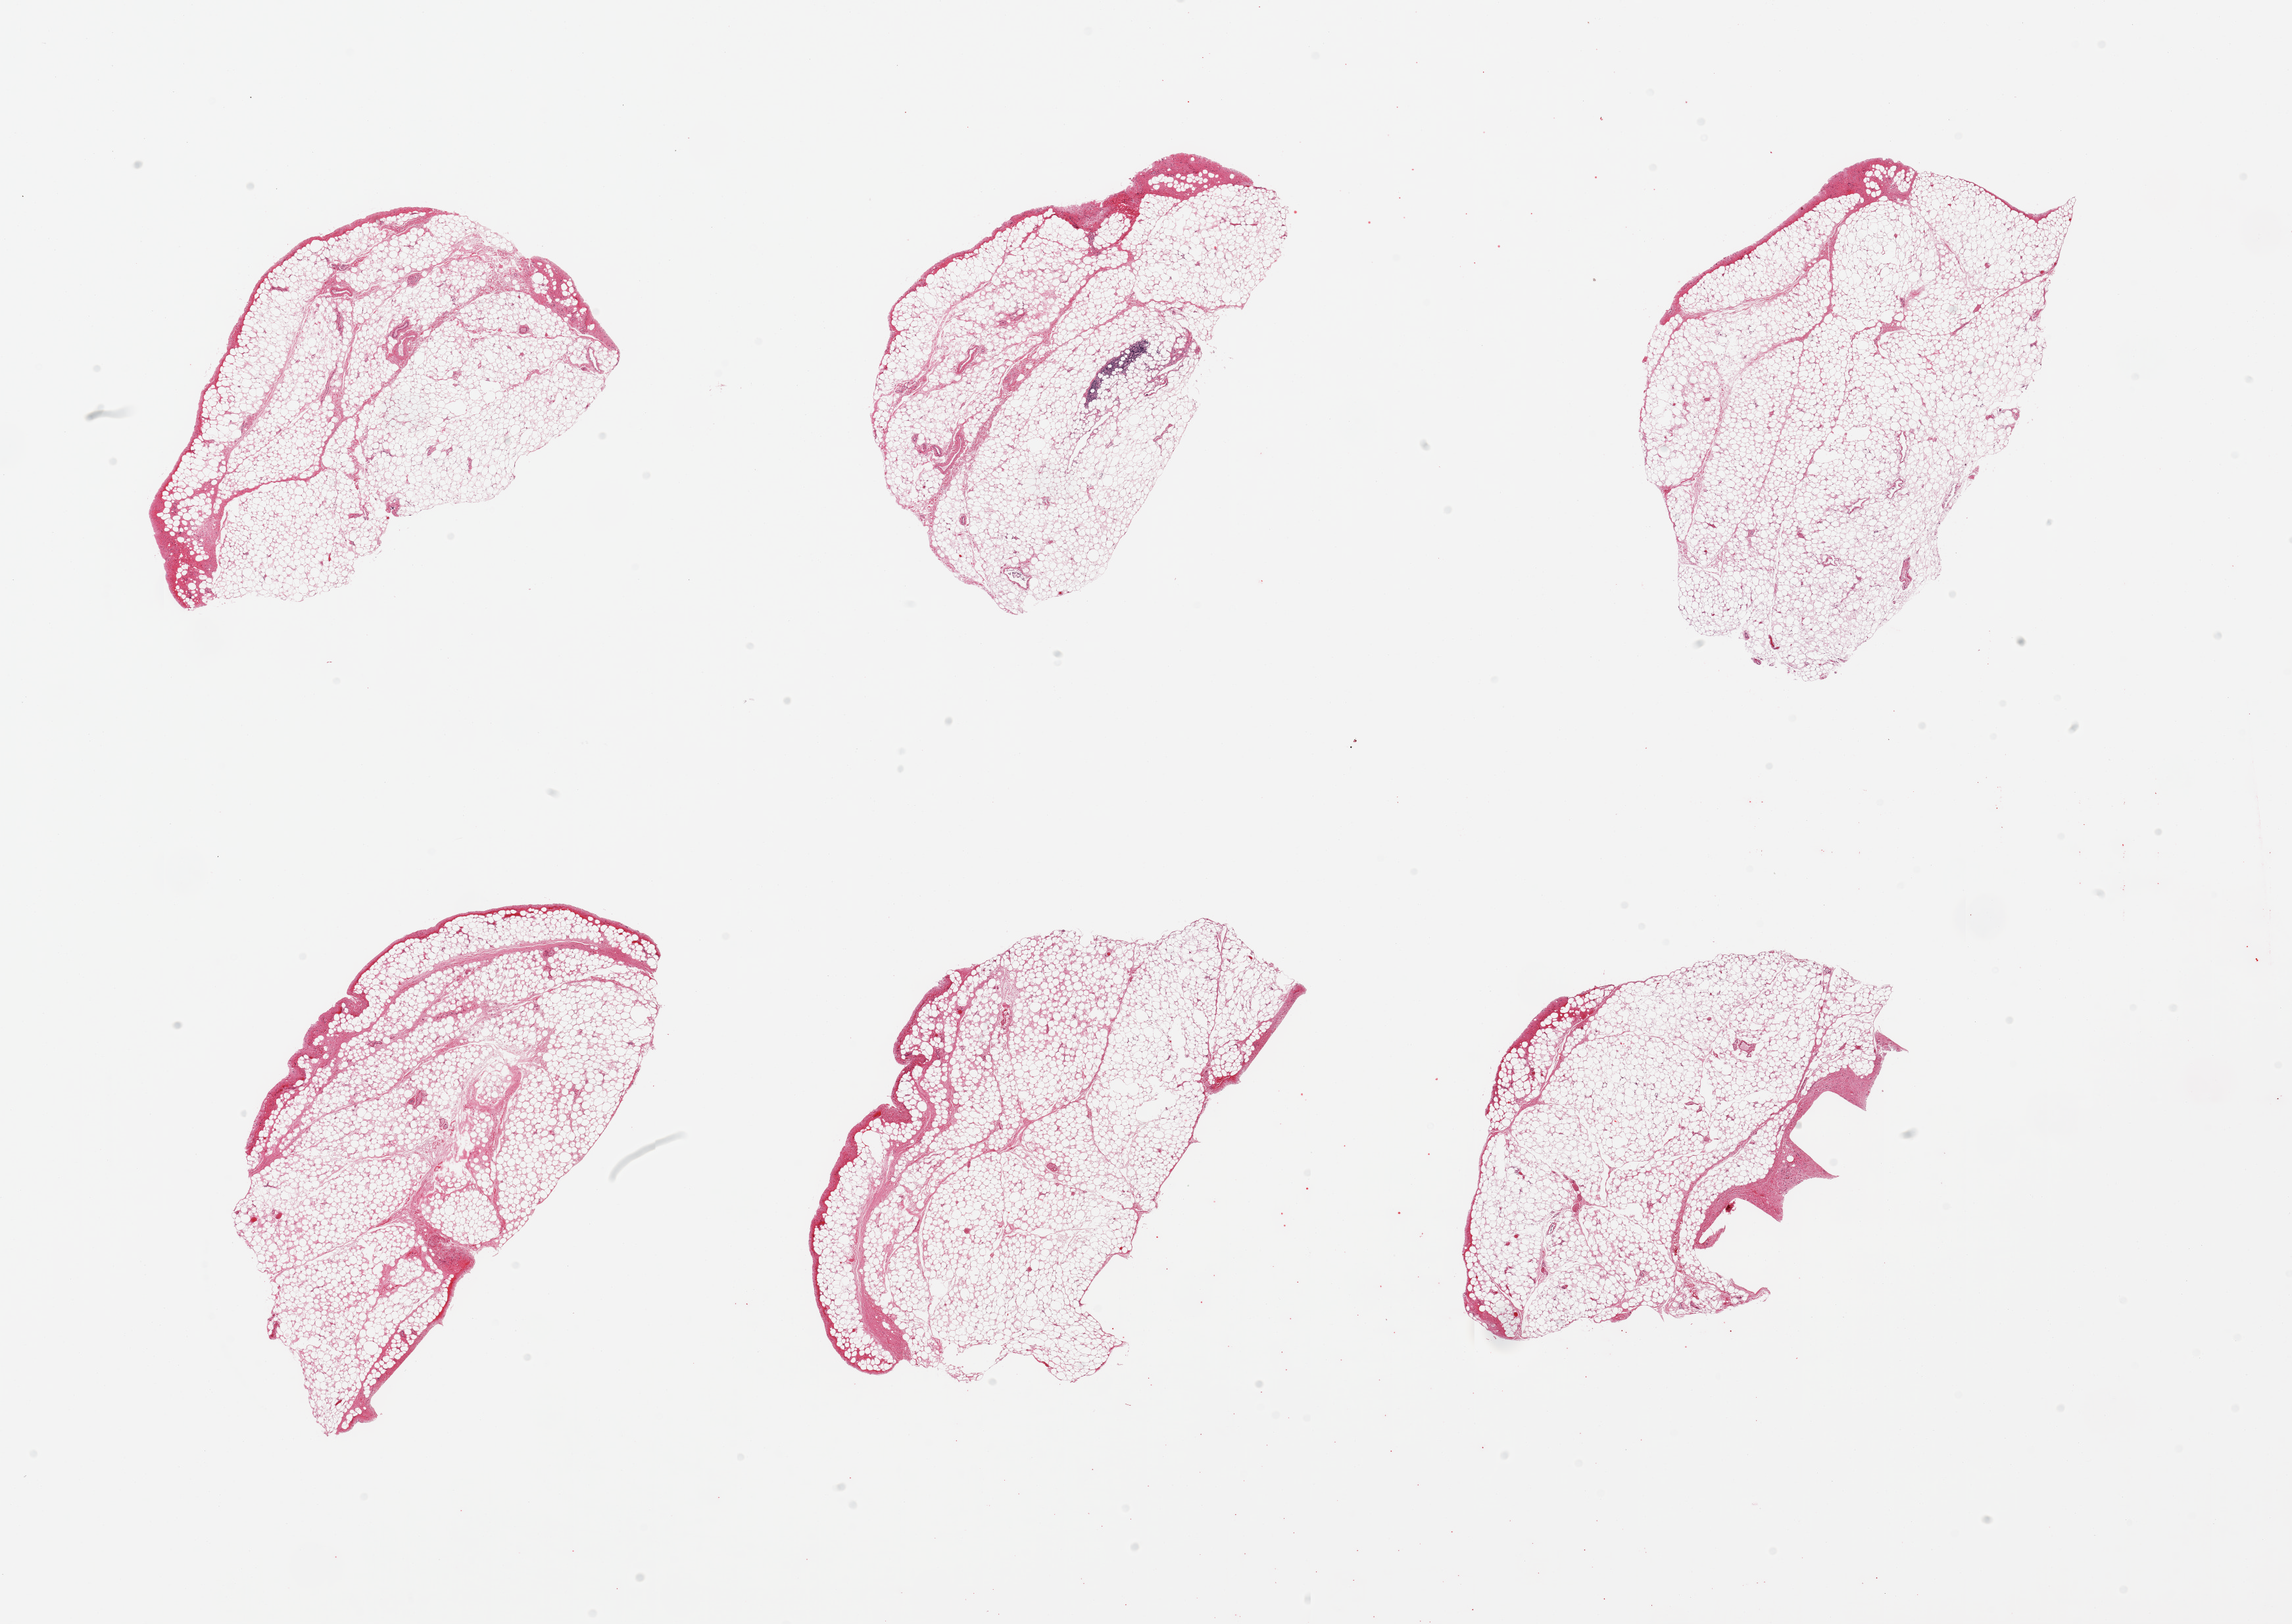
Whole-slide image, haematoxylin and eosin stain, whole scanned area (about 27.6 x 19.5 mm, slide scanned at 20x) shown as a low-resolution overview. PAXgene-fixed paraffin-embedded (PFPE) section. Section of gastroesophageal junction (target tissue). Tissue donor sample. Male donor.
Review note (as recorded): 6 pieces; adipose tissue, not muscle.